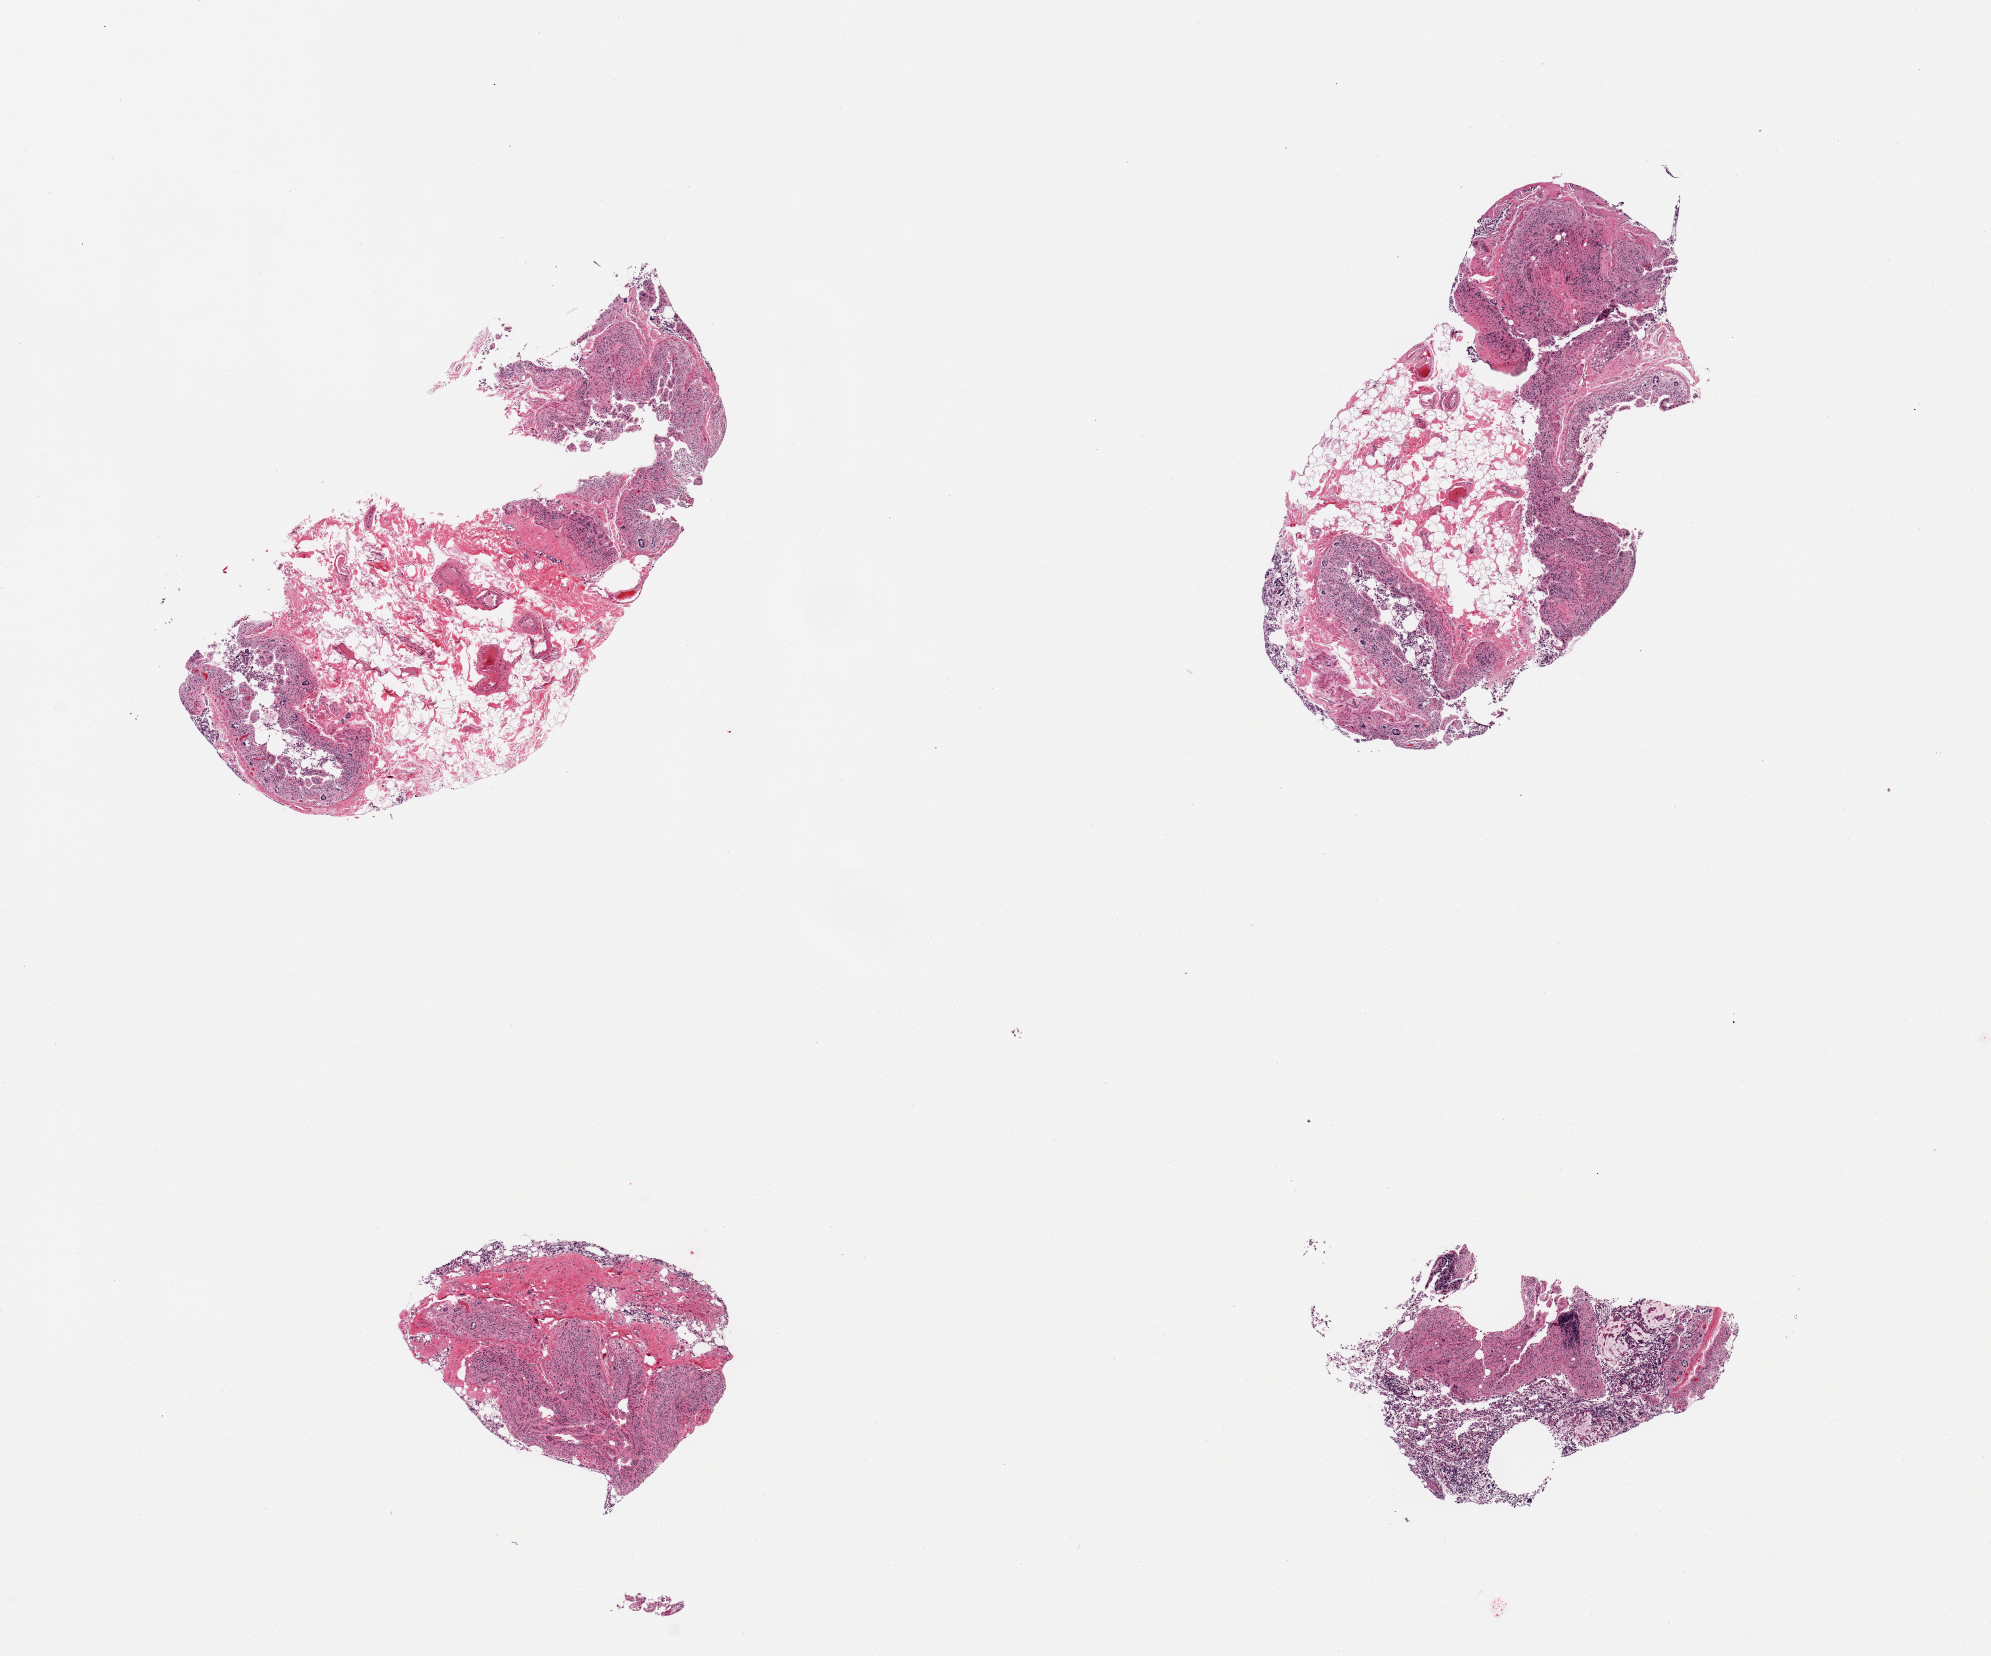
Whole-slide image, haematoxylin and eosin stain — low-resolution overview of the scanned area, about 15.8 x 13.1 mm (acquisition: 20x scan); PAXgene-fixed, paraffin-embedded tissue; sampled site (target tissue): ileum; donor tissue sample. Donor: female.
• review note (as recorded): 4 pieces; autolyzed mucosa and insufficient lymphoid tissue